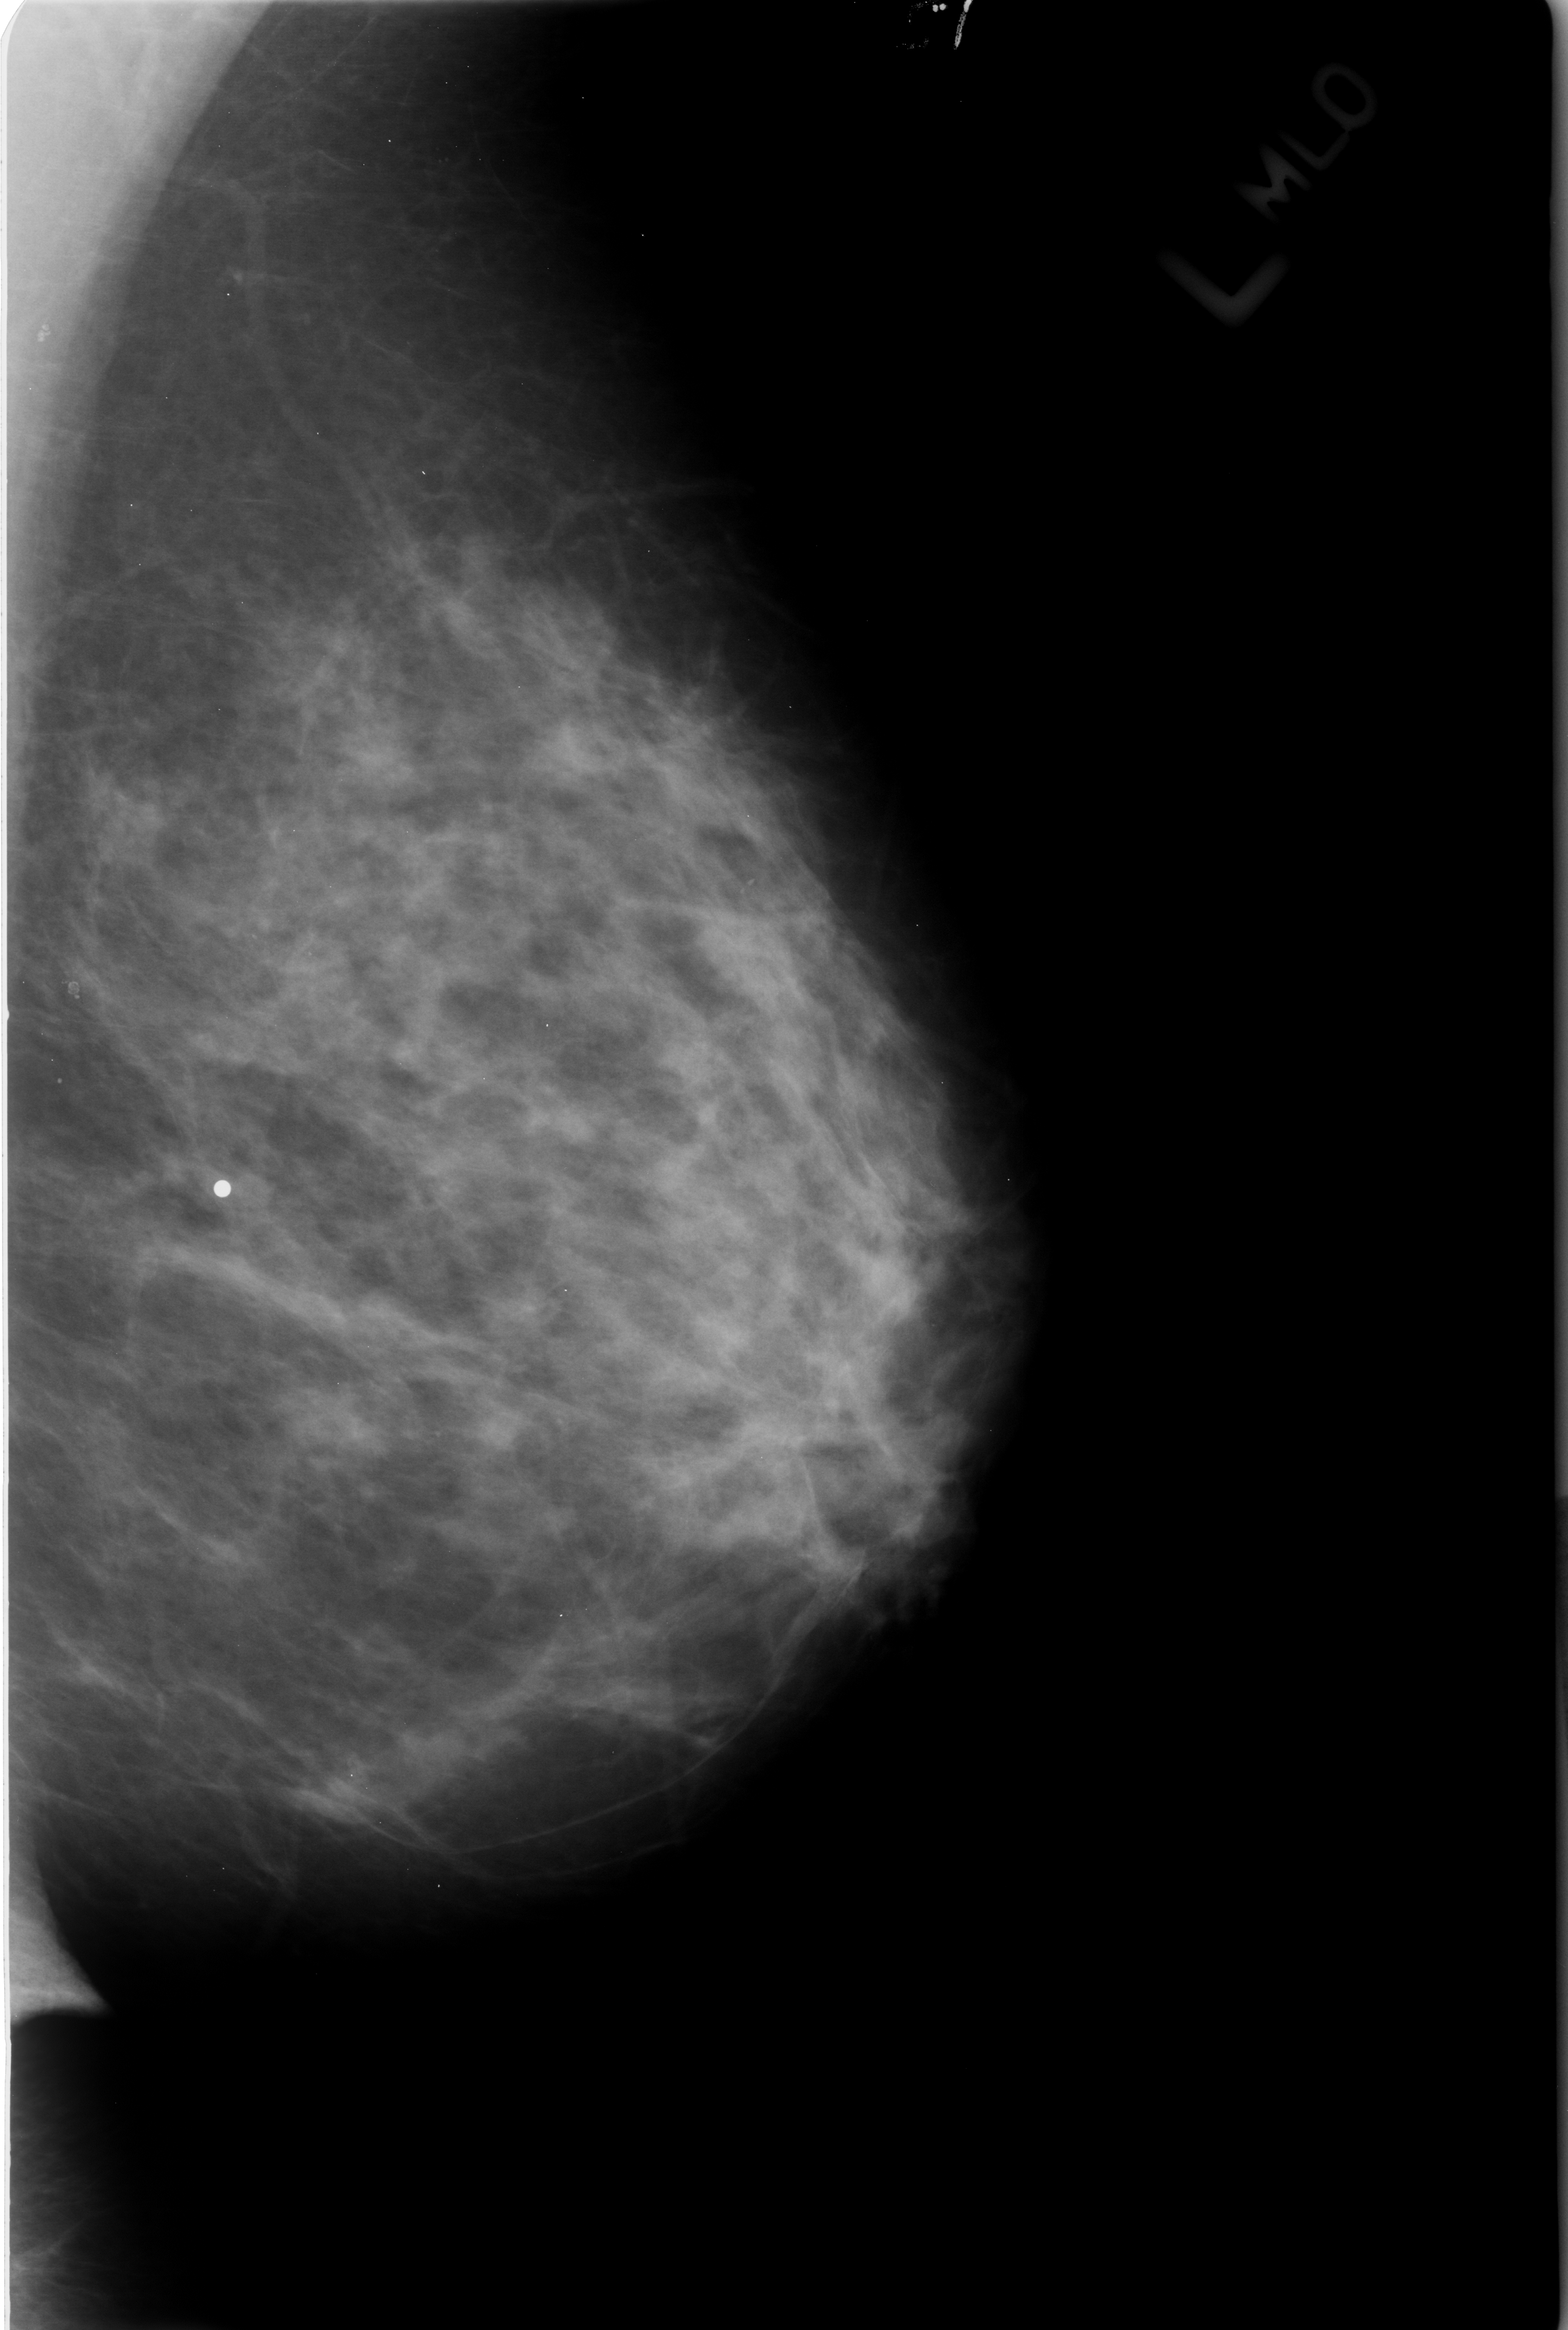
Scanned film-screen mammogram; left breast; mediolateral oblique (MLO) view; BI-RADS breast density category 3 (scale 1–4).
Calcifications, morphology lucent center; BI-RADS assessment category 2; subtlety rating 3 on a 1 (subtle) to 5 (obvious) scale; benign; no additional work-up was recommended (benign without callback).